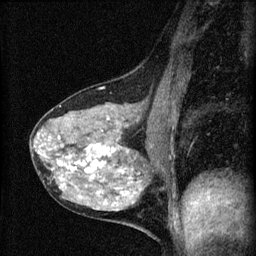
Breast MRI (dynamic contrast-enhanced), one sagittal slice. Slice 28 of 60 in the series (ordered by position). Dynamic contrast-enhanced series, image 2 of 4 at this slice position (ordered by acquisition). 1.5 T. TE 4.2 ms, TR 8.2 ms. 2 mm slice thickness. 256 × 256 image matrix. Patient: female, 41 years.
Annotated regions visible in this slice (semi-automatic segmentation, software-assisted and operator-edited):
- analysis volume of interest (the breast-tissue region the enhancement analysis was run in; not a lesion): box from (x=30, y=91) to (x=166, y=210) px
- tumour enhancement mask (voxels above the 70 % enhancement threshold inside the analysis volume of interest): (x=36, y=123)–(x=135, y=204)